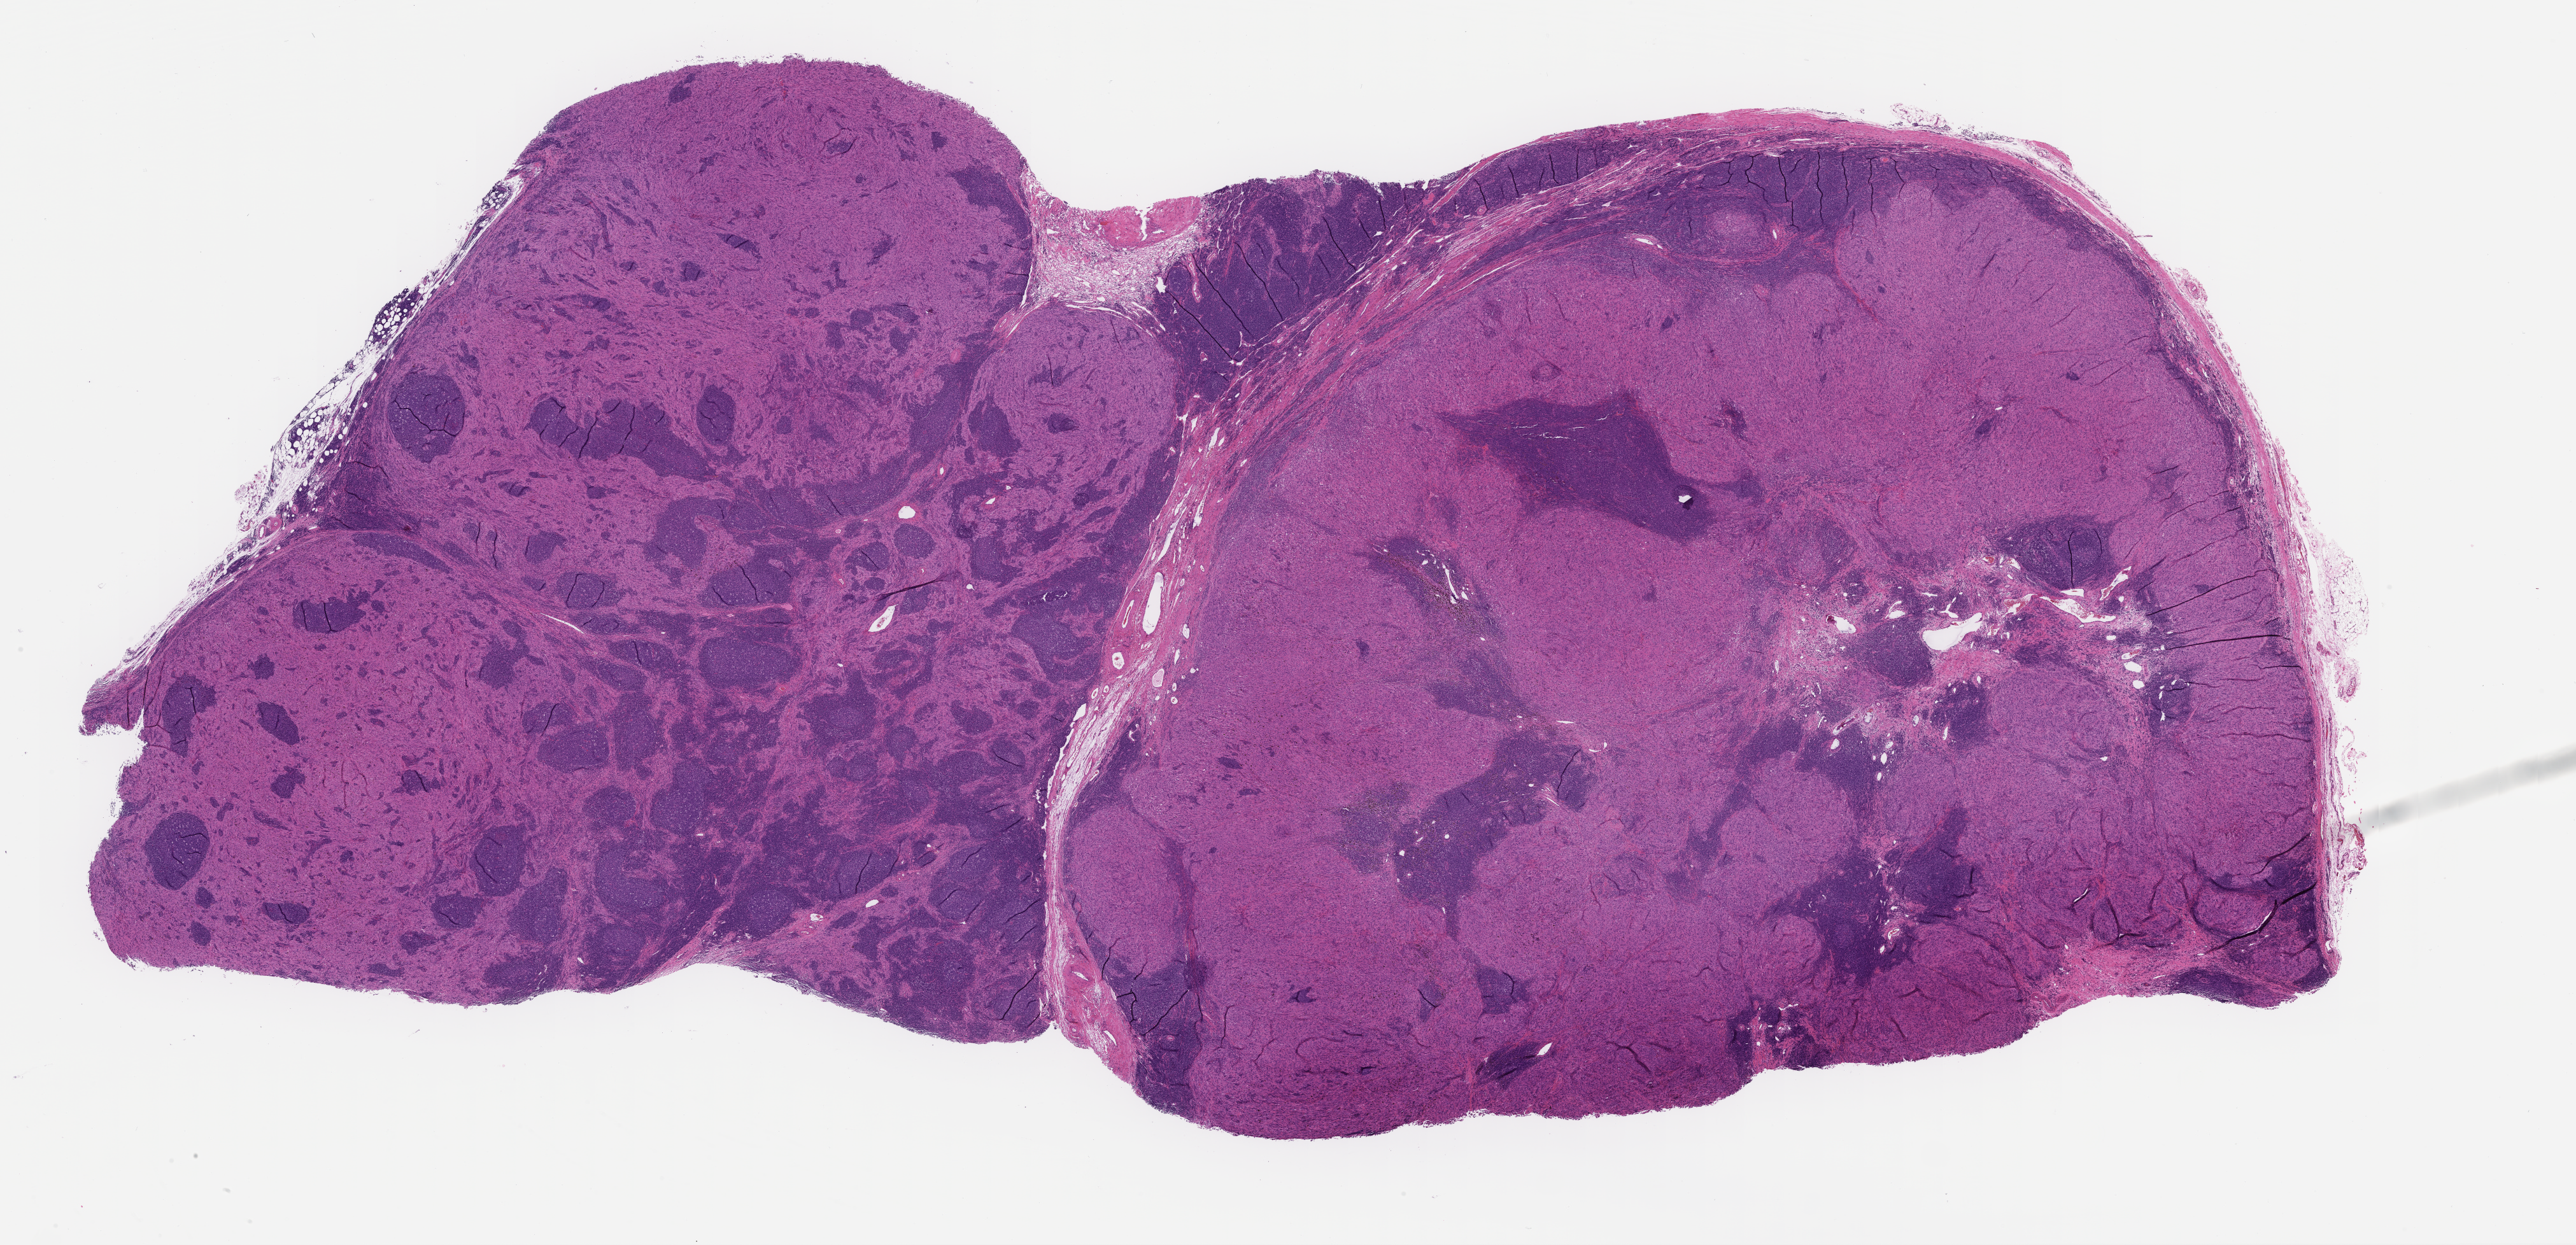
Digitized H&E-stained section — whole scanned area (about 32.7 x 15.8 mm) shown as a low-resolution overview. FFPE section. Specimen time point: collected at baseline (before treatment). Patient sex: female.
This section: metastatic tumor tissue. Primary diagnosis of the patient: Melanoma.